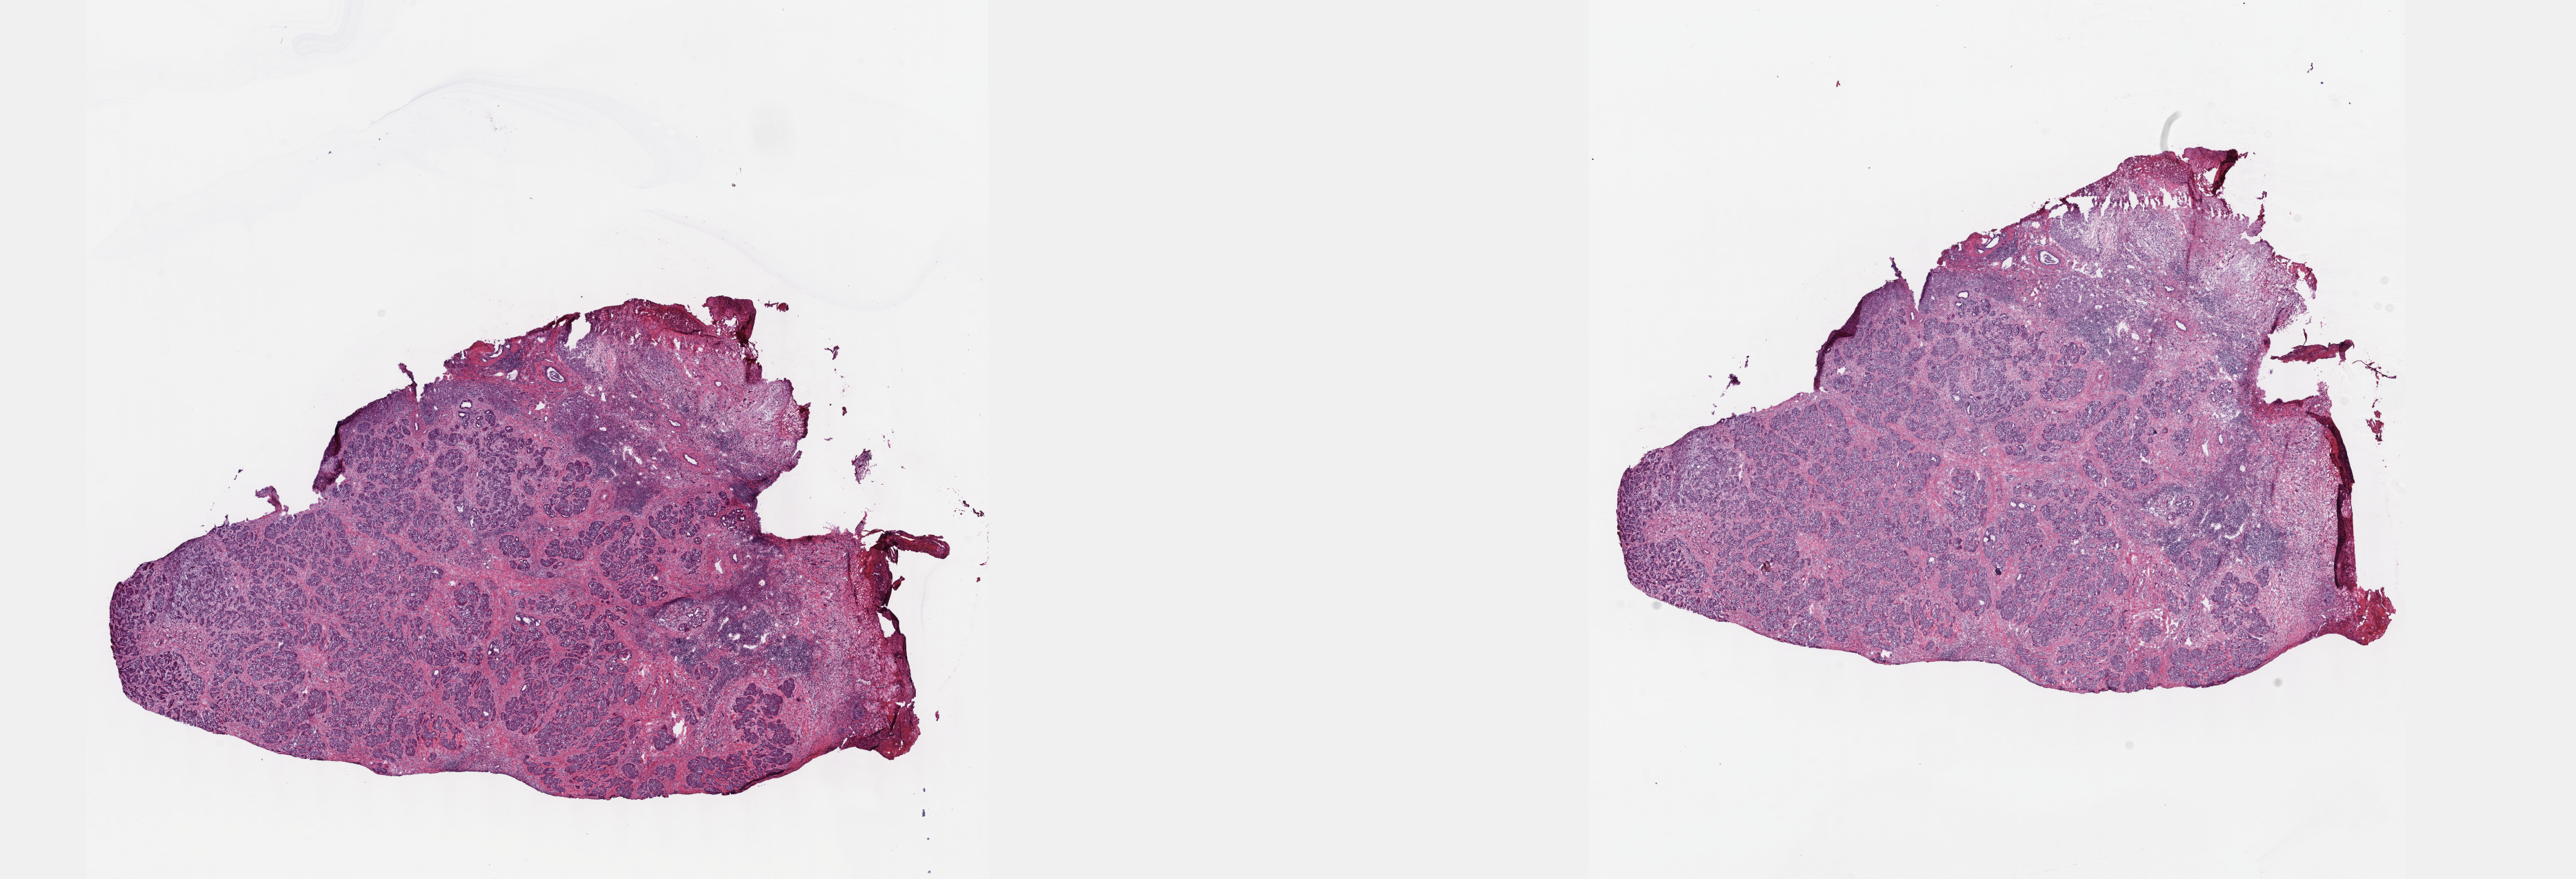
Whole-slide histology image, H&E, shown as a low-resolution overview of the whole scanned area (about 30.2 x 10.3 mm); frozen section from the top of the tissue portion; primary tumour sample from the bile duct. Male, age 60 years at initial diagnosis. Slide review estimates, as recorded: tumour cells 100%, tumour nuclei 70%.
Pathologic diagnosis: Cholangiocarcinoma (intrahepatic bile duct).